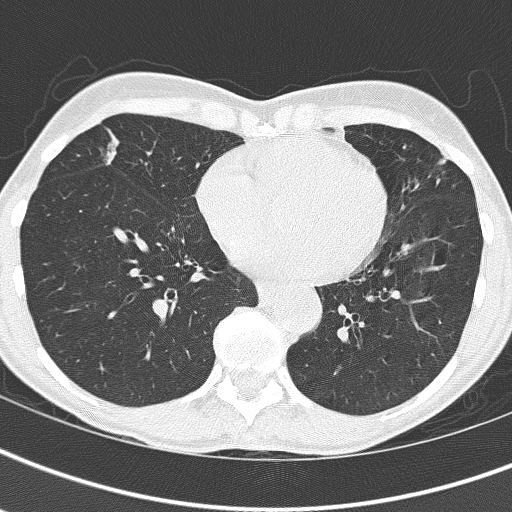
Low-dose screening chest CT, axial slice; first (baseline) screen; lung window (W 1500 / L -600 HU); 2 mm slice thickness; lung (sharp) reconstruction kernel (B60f); 120 kVp; slice 101 of 161 in the series. Female, age 67 years at enrolment. Current smoker at enrolment.
Expert reader's lesion annotation, box from (x=83, y=119) to (x=179, y=201) px. Screening reader's record for this exam: no non-calcified nodule ≥4 mm recorded. Official screen result: negative screen, significant abnormalities not suspicious for lung cancer. Later outcome: lung cancer diagnosed 832 days after this screen — bronchiolo-alveolar adenocarcinoma, NOS, right middle lobe, well differentiated (G1), stage IA (AJCC 6th edition), 25 mm at pathology.